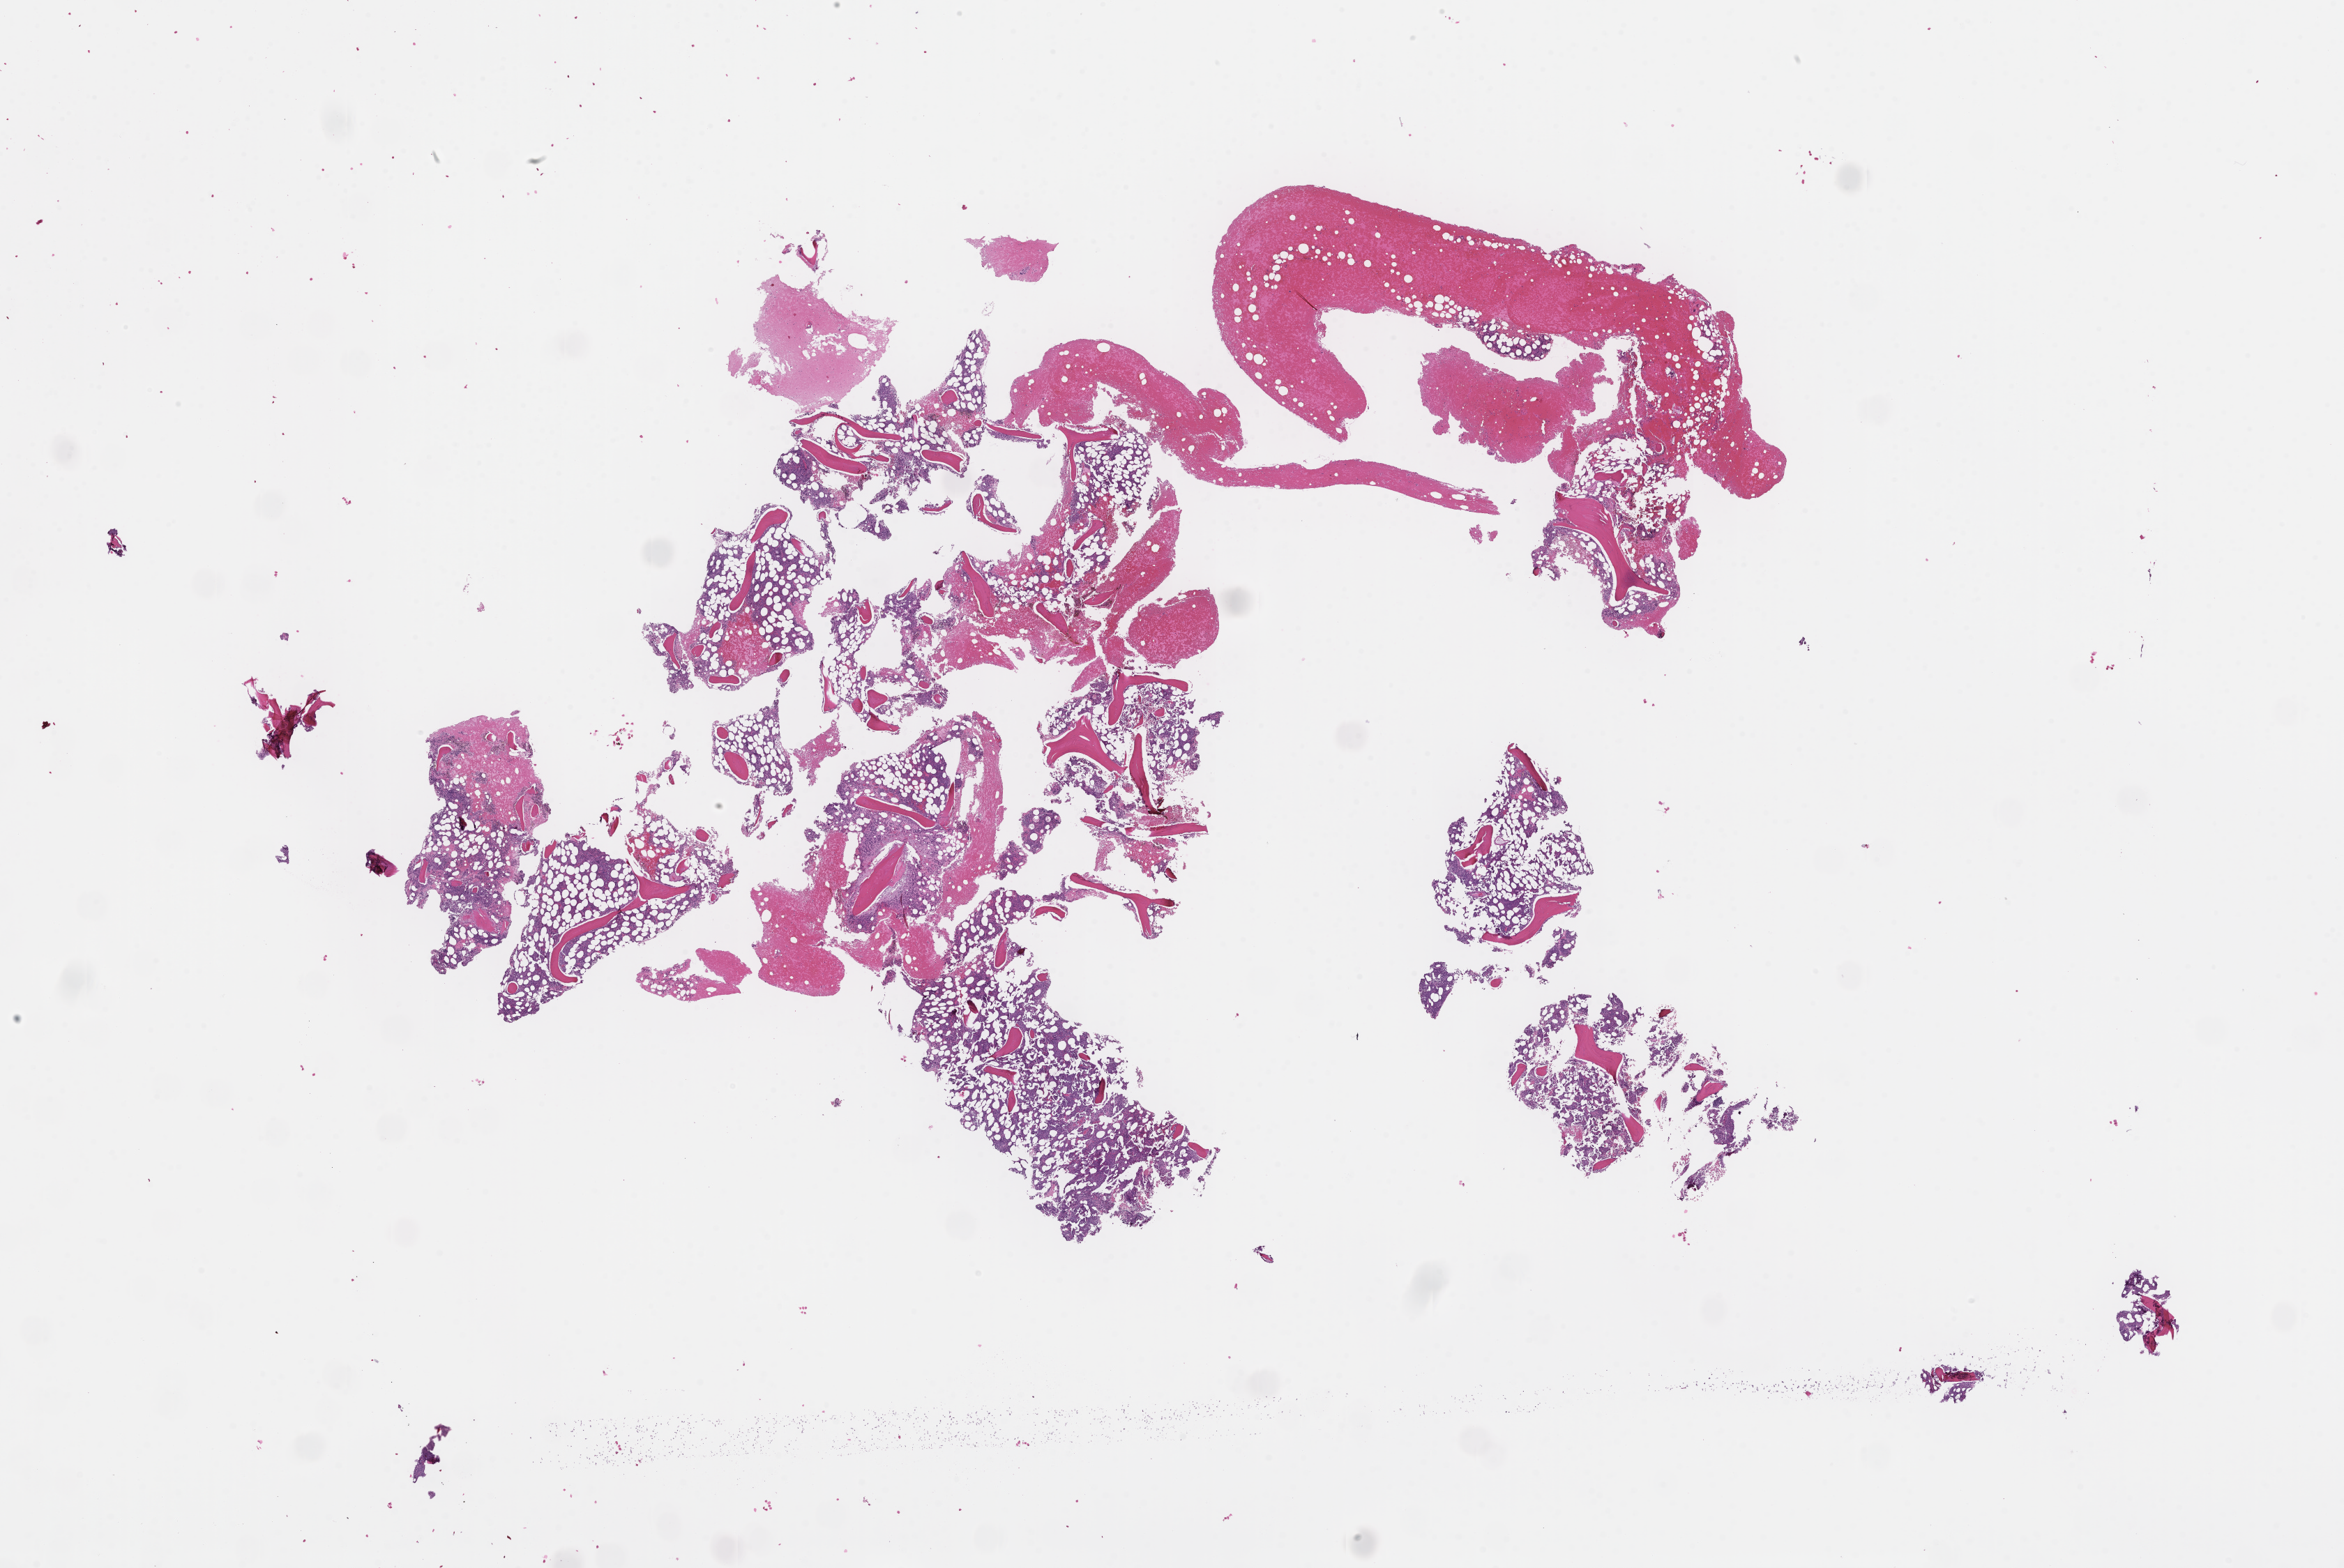
Hematoxylin and eosin (H&E) whole-slide image, shown as a low-resolution overview of the whole scanned area (about 27.1 x 18.2 mm), FFPE section, tissue site: bone marrow. Male patient.
• this section: primary tumour tissue
• diagnosis: Plasma Cell Myeloma